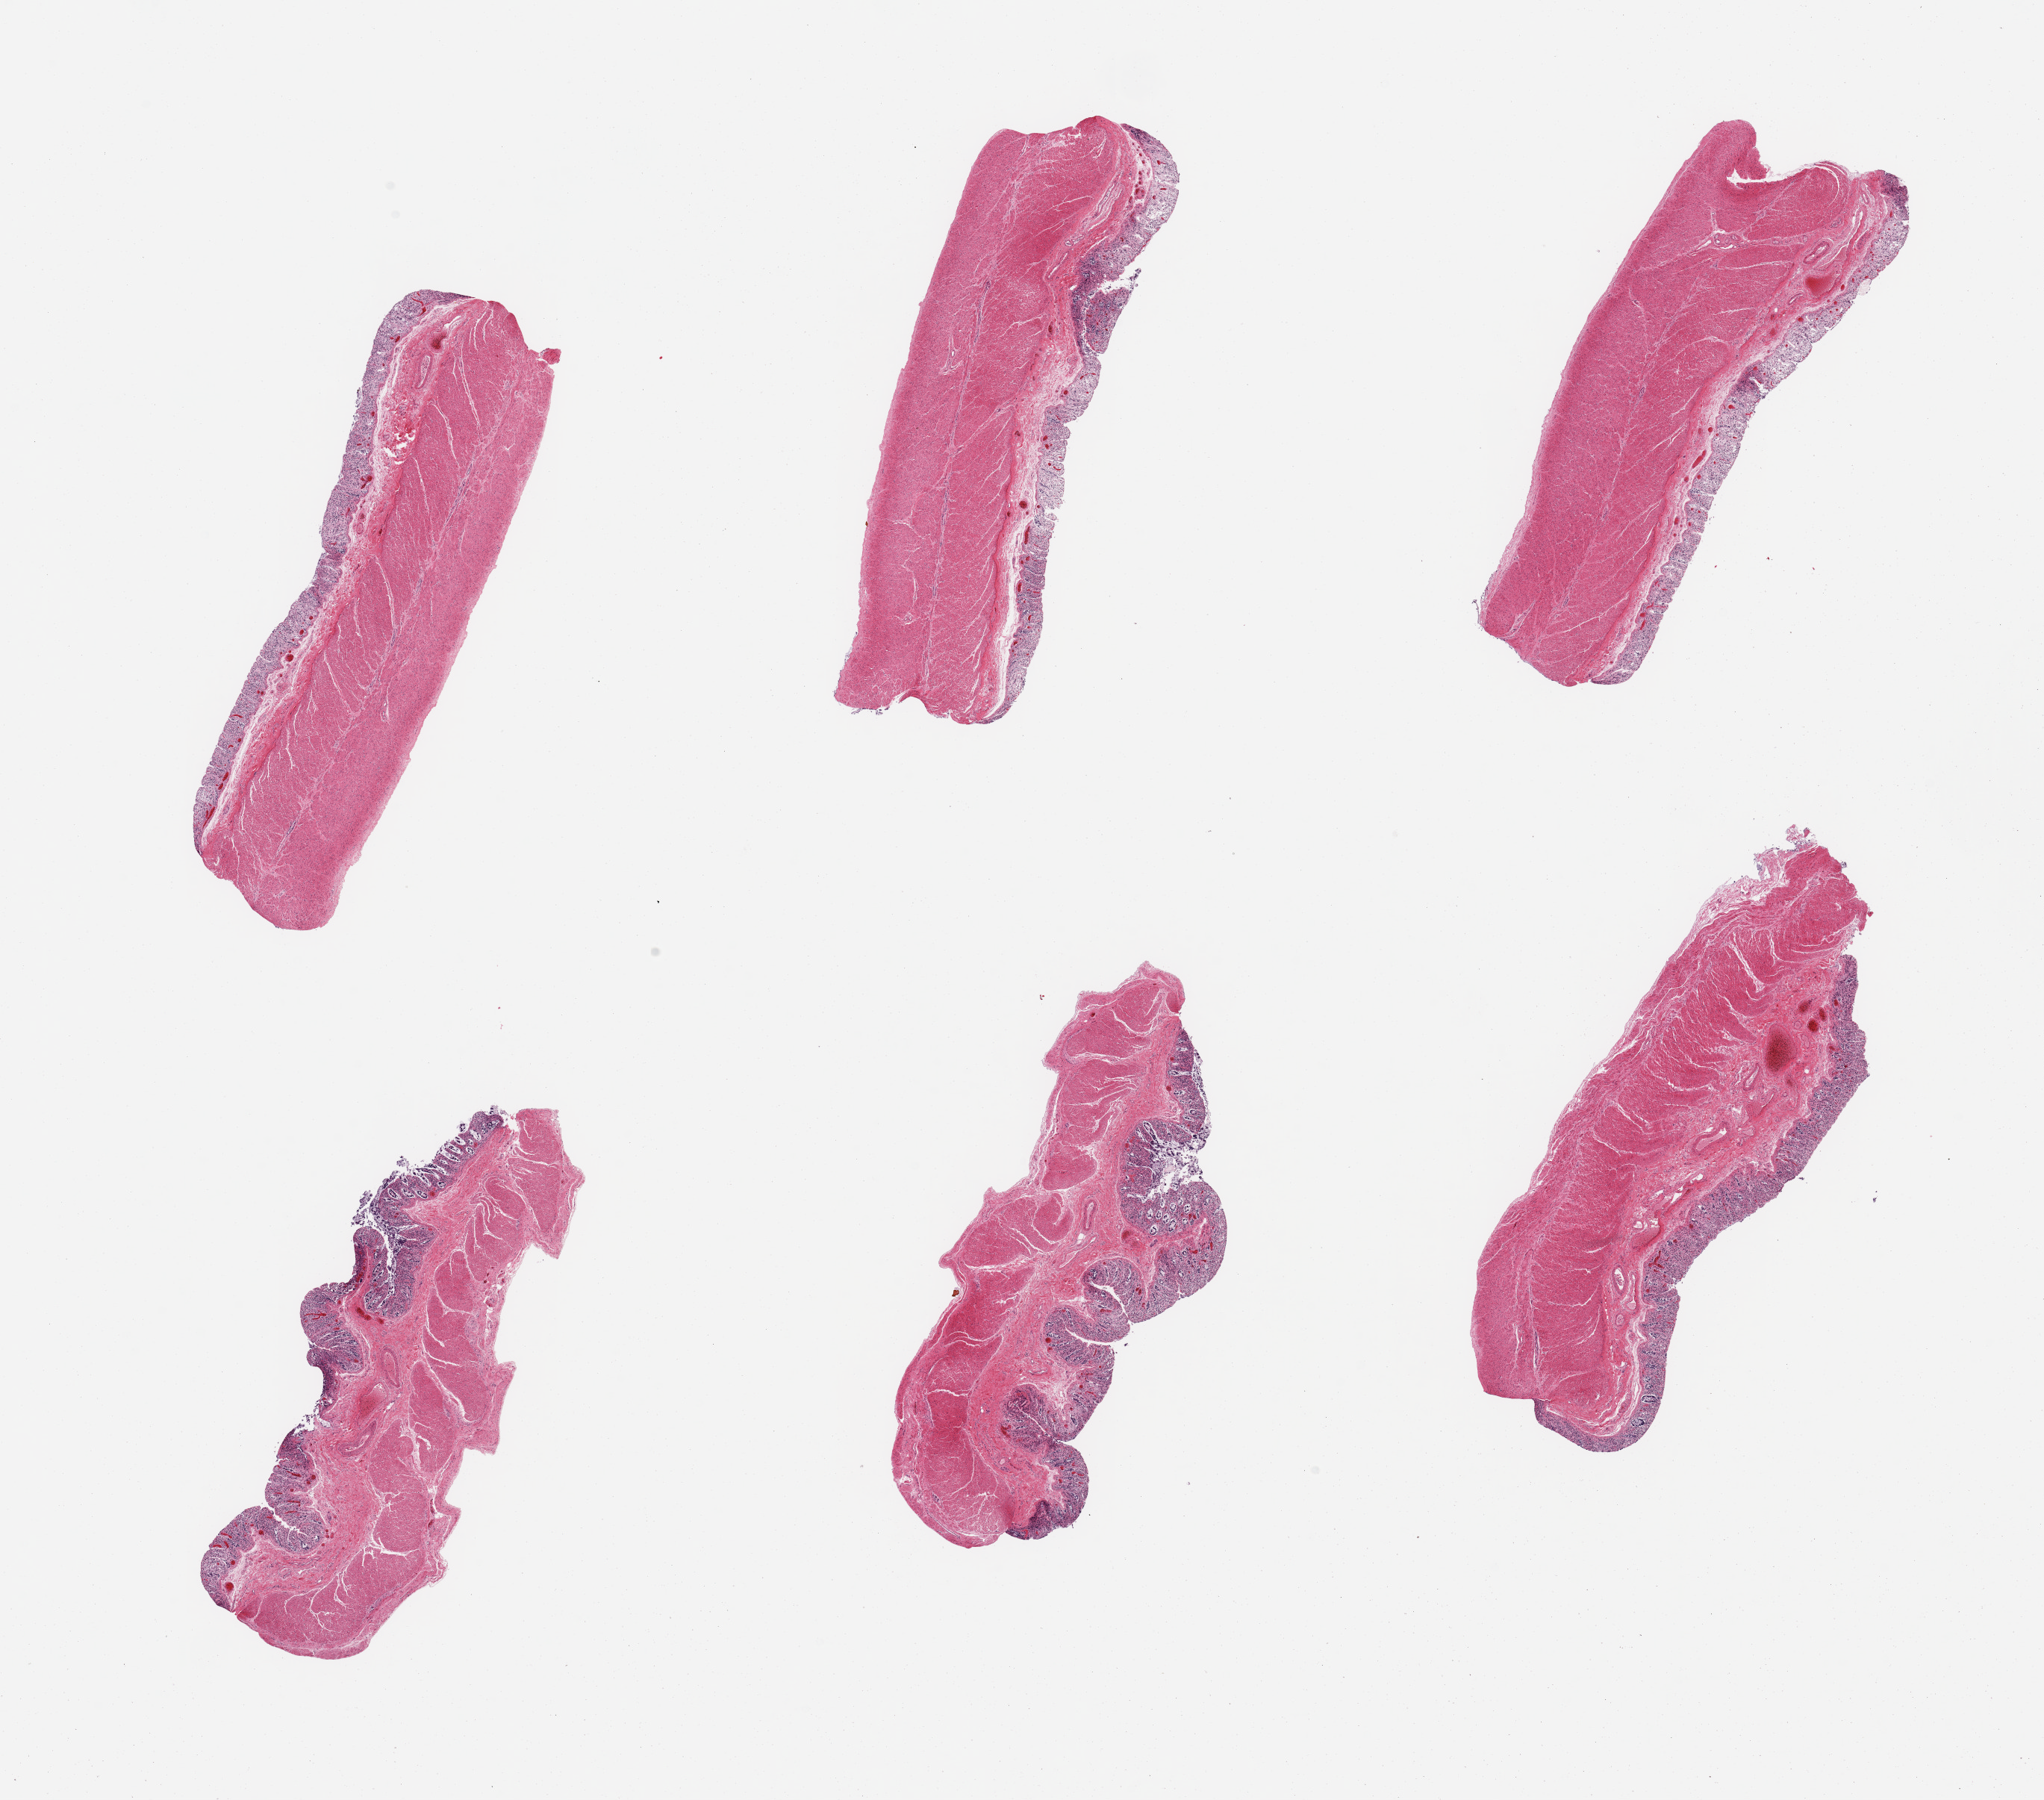
Haematoxylin and eosin whole-slide image, a low-resolution overview of the entire scanned area, about 21.7 x 19.1 mm (slide scanned at 20x), PAXgene-fixed paraffin-embedded (PFPE) section, section of transverse colon (target tissue), donor tissue sample. Donor: male.
Review note (as recorded): 6 pieces; moderate to severe mucosal autolysis; congestion; preserved muscularis.